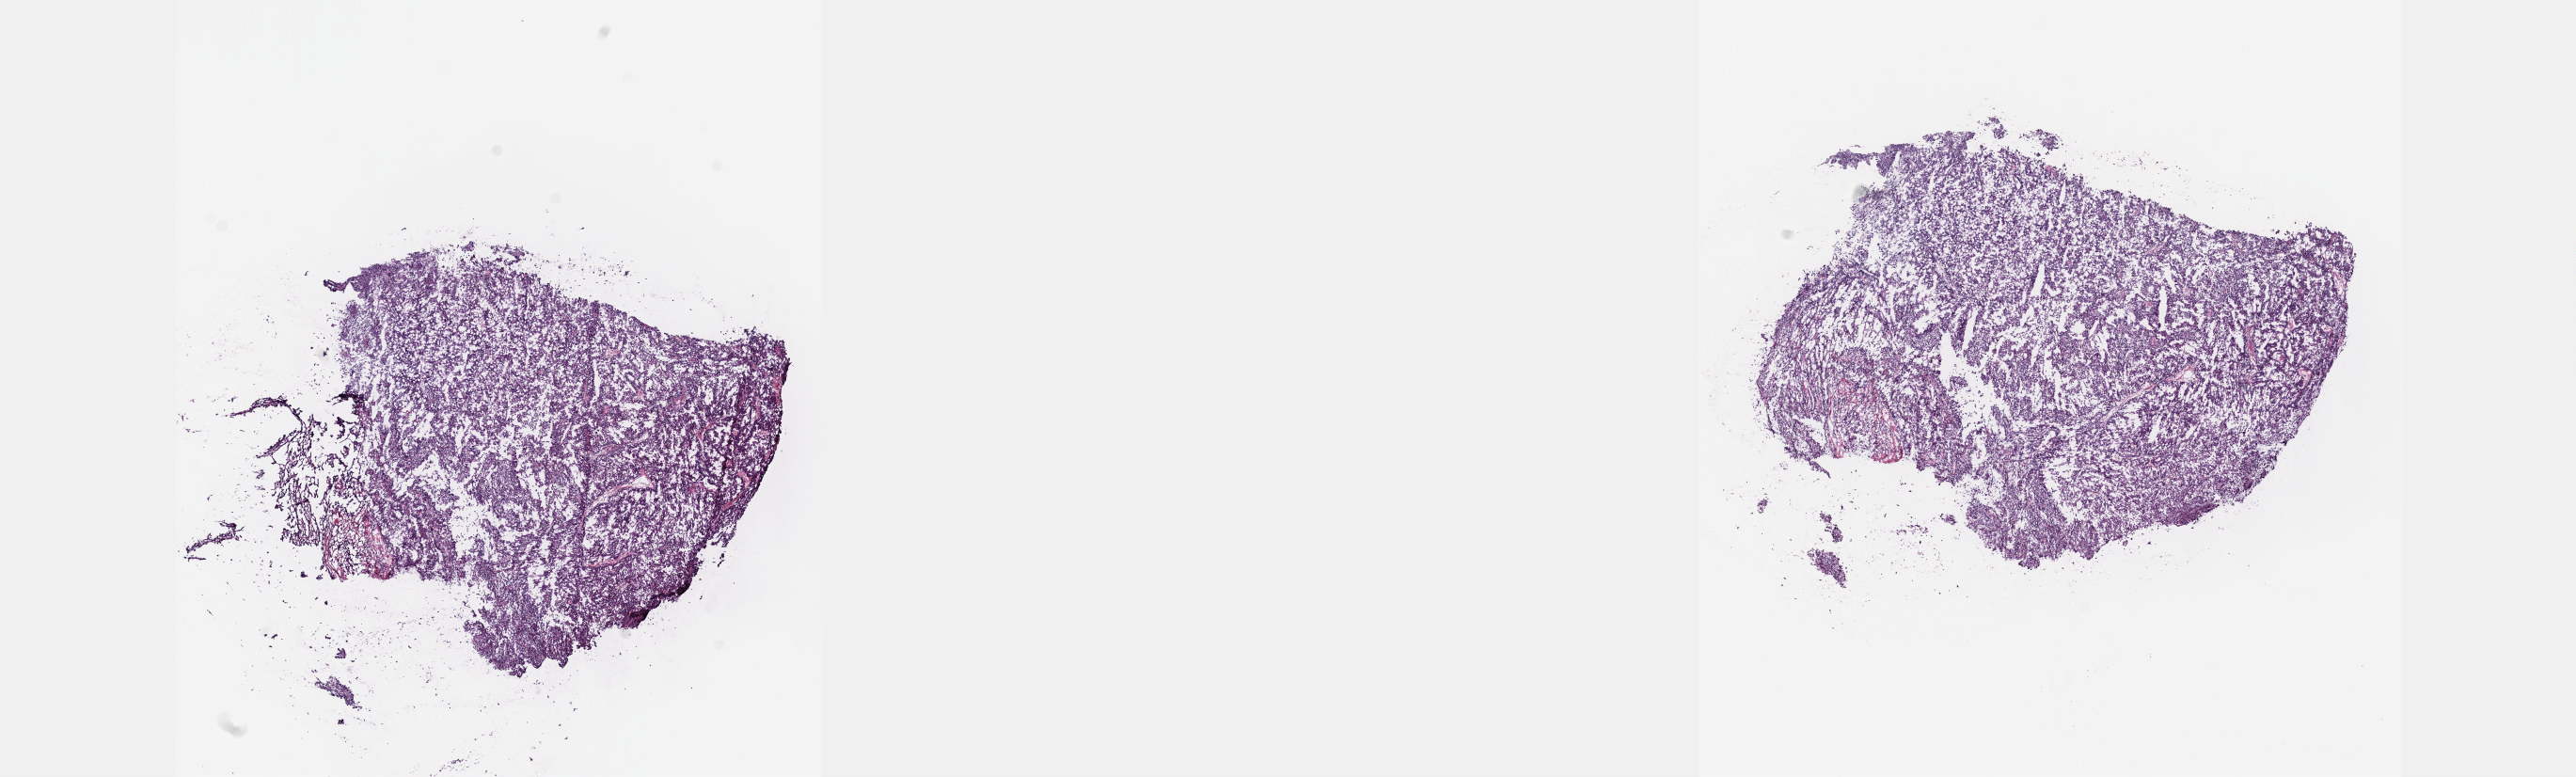
Whole-slide histology image, H&E, low-resolution overview of the scanned area, about 22.1 x 6.7 mm (slide scanned at 40x); frozen section; primary tumour sample from the kidney. Patient: male, age at initial diagnosis 55 years. Composition of this section per pathologist review: tumour cells 100%, tumour nuclei 75%, normal cells 0%, stromal cells 0%, necrosis 0%. Inflammatory infiltration, as recorded: lymphocyte infiltration 4%, monocyte infiltration 2%, neutrophil infiltration 0%.
Pathologic diagnosis: Papillary adenocarcinoma, NOS. AJCC pathologic stage: I (7th edition).